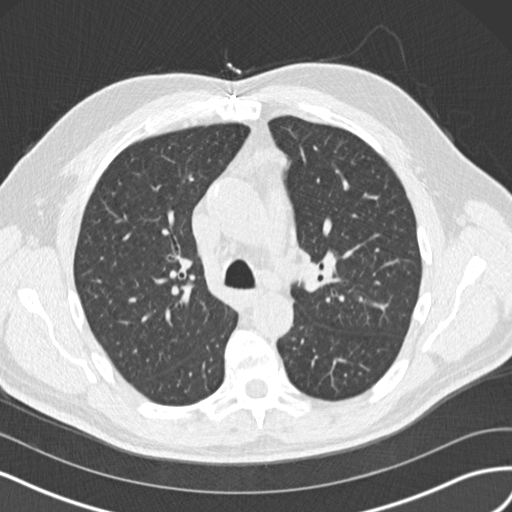
Axial slice from a low-dose chest CT screening exam, baseline annual screen, lung window (W 1500 / L -600 HU), standard (soft-tissue) reconstruction kernel (B30f), slice 53 of 160 in the series, 512 × 512 image matrix, field of view 360 × 360 mm. Male participant, aged 65 years at enrolment. Former smoker at enrolment.
Lesion marked by an expert reader, bounding box (x1, y1, x2, y2) in pixels: (303, 243, 353, 297). The screening reader recorded 4 non-calcified nodules or masses ≥4 mm on this exam (left upper lobe, left upper lobe, right upper lobe, right middle lobe); which of them this box marks is not recorded. Participant outcome: lung cancer diagnosed 945 days after this screen — acinar cell carcinoma, left upper lobe, stage IA (AJCC 6th edition), 25 mm at pathology.